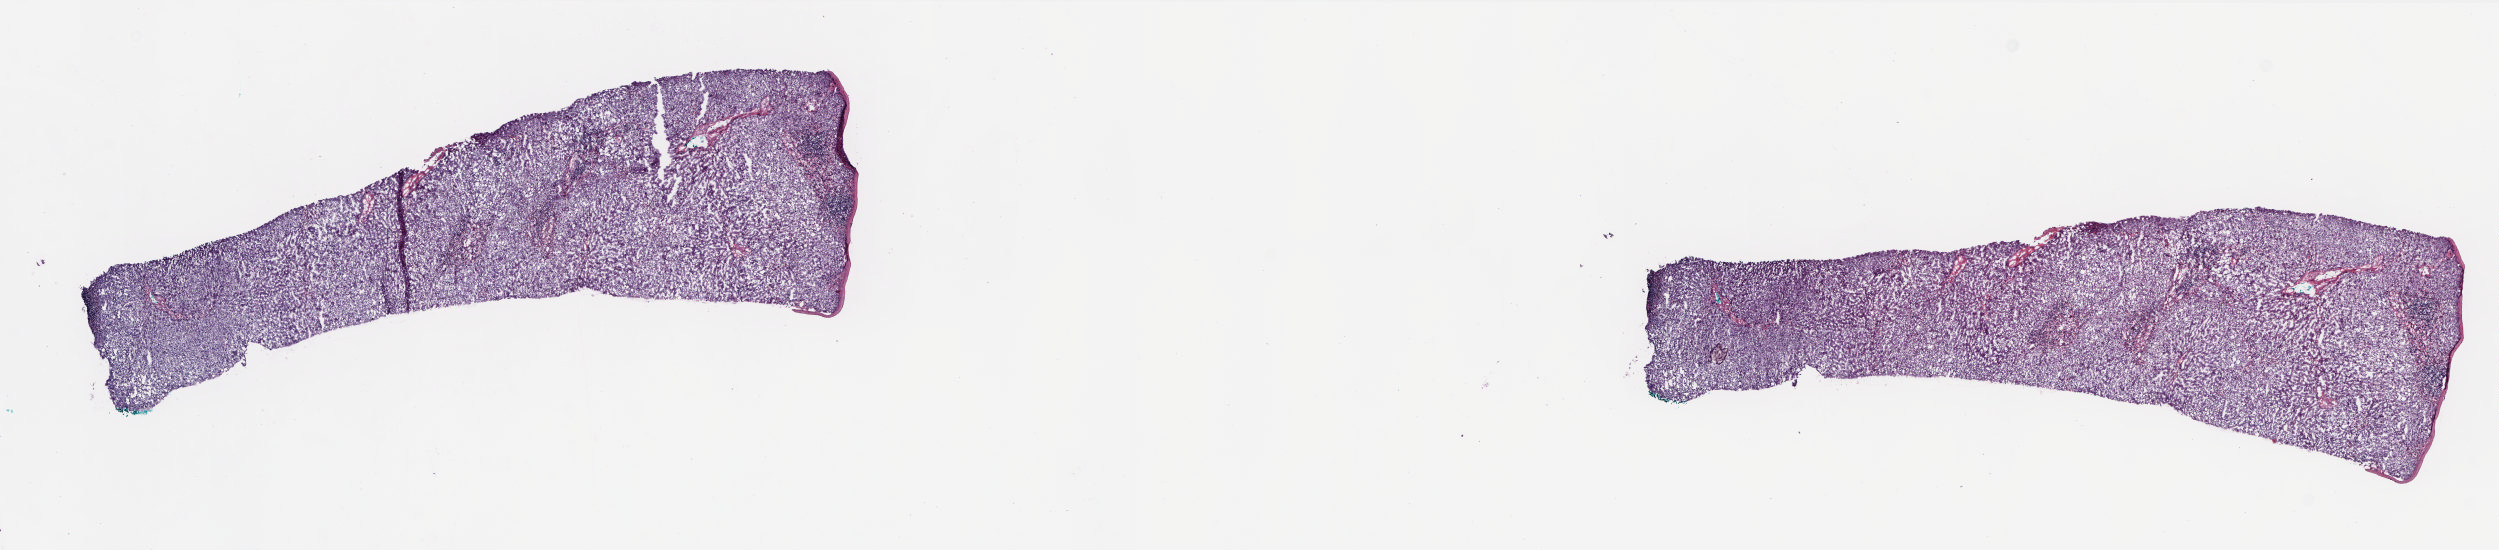
Whole-slide histology image, H&E, whole scanned area (about 20.0 x 4.4 mm, from a 20x scan) shown as a low-resolution overview; frozen section; sample: solid tissue normal (non-tumour tissue), liver. Female patient; age at initial diagnosis 51 years. Composition of this section per pathologist review: tumour cells 0%, tumour nuclei 0%, normal cells 90%, stromal cells 10%, necrosis 0%. Infiltration values recorded for this section: lymphocyte infiltration 4%, monocyte infiltration 1%, neutrophil infiltration 0%.
This section: solid tissue normal (non-tumour) sample from the same patient. Patient diagnosis: Hepatocellular carcinoma, NOS.